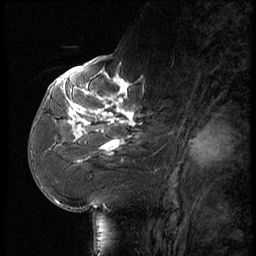
Breast MRI (dynamic contrast-enhanced), one sagittal slice; slice 29 of 56 in the series (ordered by position); dynamic contrast-enhanced series, image 2 of 3 at this slice position (ordered by acquisition); 1.5 T; TE 4.2 ms, TR 9 ms; 256 × 256 image matrix. Female patient, age 61 years. Case-level facts recorded for this patient, not image findings: setting: breast cancer imaged before/during neoadjuvant chemotherapy; receptor status: HR-positive, HER2-negative.
Annotated regions visible in this slice (semi-automatic segmentation, software-assisted and operator-edited):
- analysis volume of interest (the breast-tissue region the enhancement analysis was run in; not a lesion): bounding box [x1, y1, x2, y2] px = [65, 74, 167, 175]
- tumour enhancement mask (voxels above the 140 % enhancement threshold inside the analysis volume of interest): [71, 79, 135, 155]